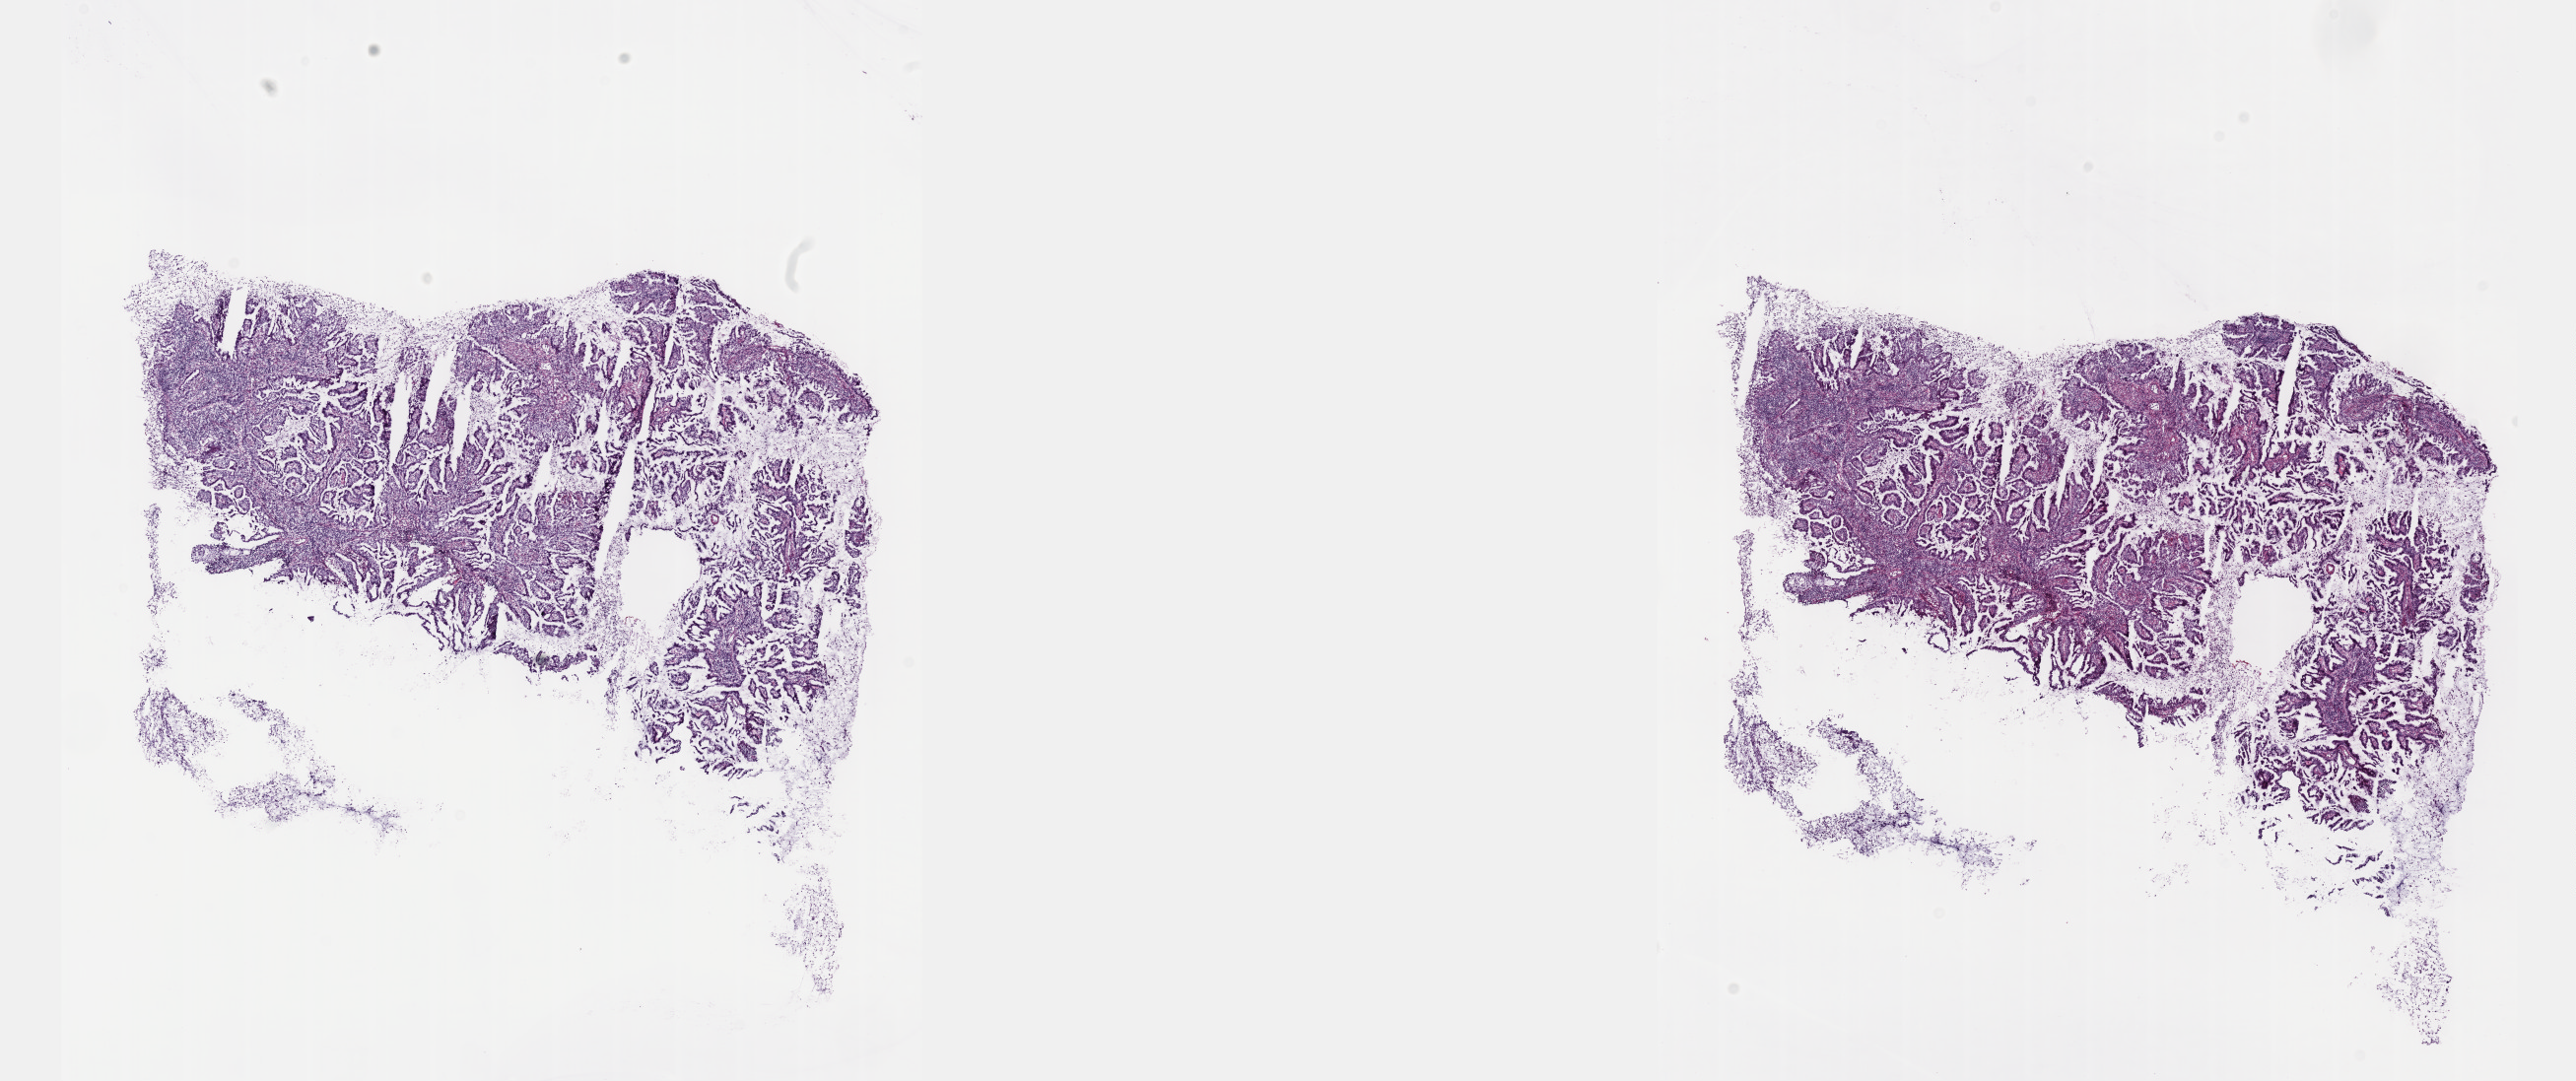
Digitized H&E tissue section (whole slide) — shown as a low-resolution overview of the whole scanned area (about 21.1 x 8.9 mm). Frozen section from the top of the tissue portion. Primary tumour sample from the cervix. Patient: female, age at initial diagnosis 46 years. Histologic grade: G2 (moderately differentiated). Pathologist review of this section (percent, as recorded): tumour cells 100%, tumour nuclei 60%, normal cells 0%, stromal cells 0%, necrosis 0%. Infiltration values recorded for this section: lymphocyte infiltration 10%, monocyte infiltration 1%, neutrophil infiltration 1%.
• diagnosis: Mucinous adenocarcinoma, endocervical type
• FIGO stage: IVB